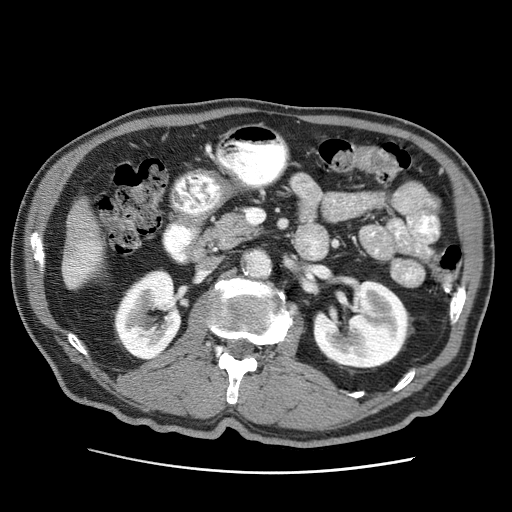
Contrast-enhanced abdominal CT (liver protocol), one axial slice; slice 8 of 75 in the series (ordered by position); reconstruction kernel STANDARD; 120 kVp; soft-tissue window (W 400 / L 40 HU); 512 × 512 image matrix, field of view 360 × 360 mm. From the clinical record (not read from this slice): diagnosis: hepatocellular carcinoma (patient treated with transarterial chemoembolisation; whether this scan precedes or follows treatment is not stated here); TNM stage (as recorded): Stage-IIIA; Child-Pugh class: A; tumour differentiation: well differentiated; tumour nodularity: multinodular.
Outlined on this slice (semi-automatically segmented with operator editing):
- liver parenchyma outside the tumour (the mass and vessels are separate outlines, so this box may not span the whole liver): bounding box [x1, y1, x2, y2] px = [62, 200, 102, 288]
- liver vessels: [70, 245, 98, 280]